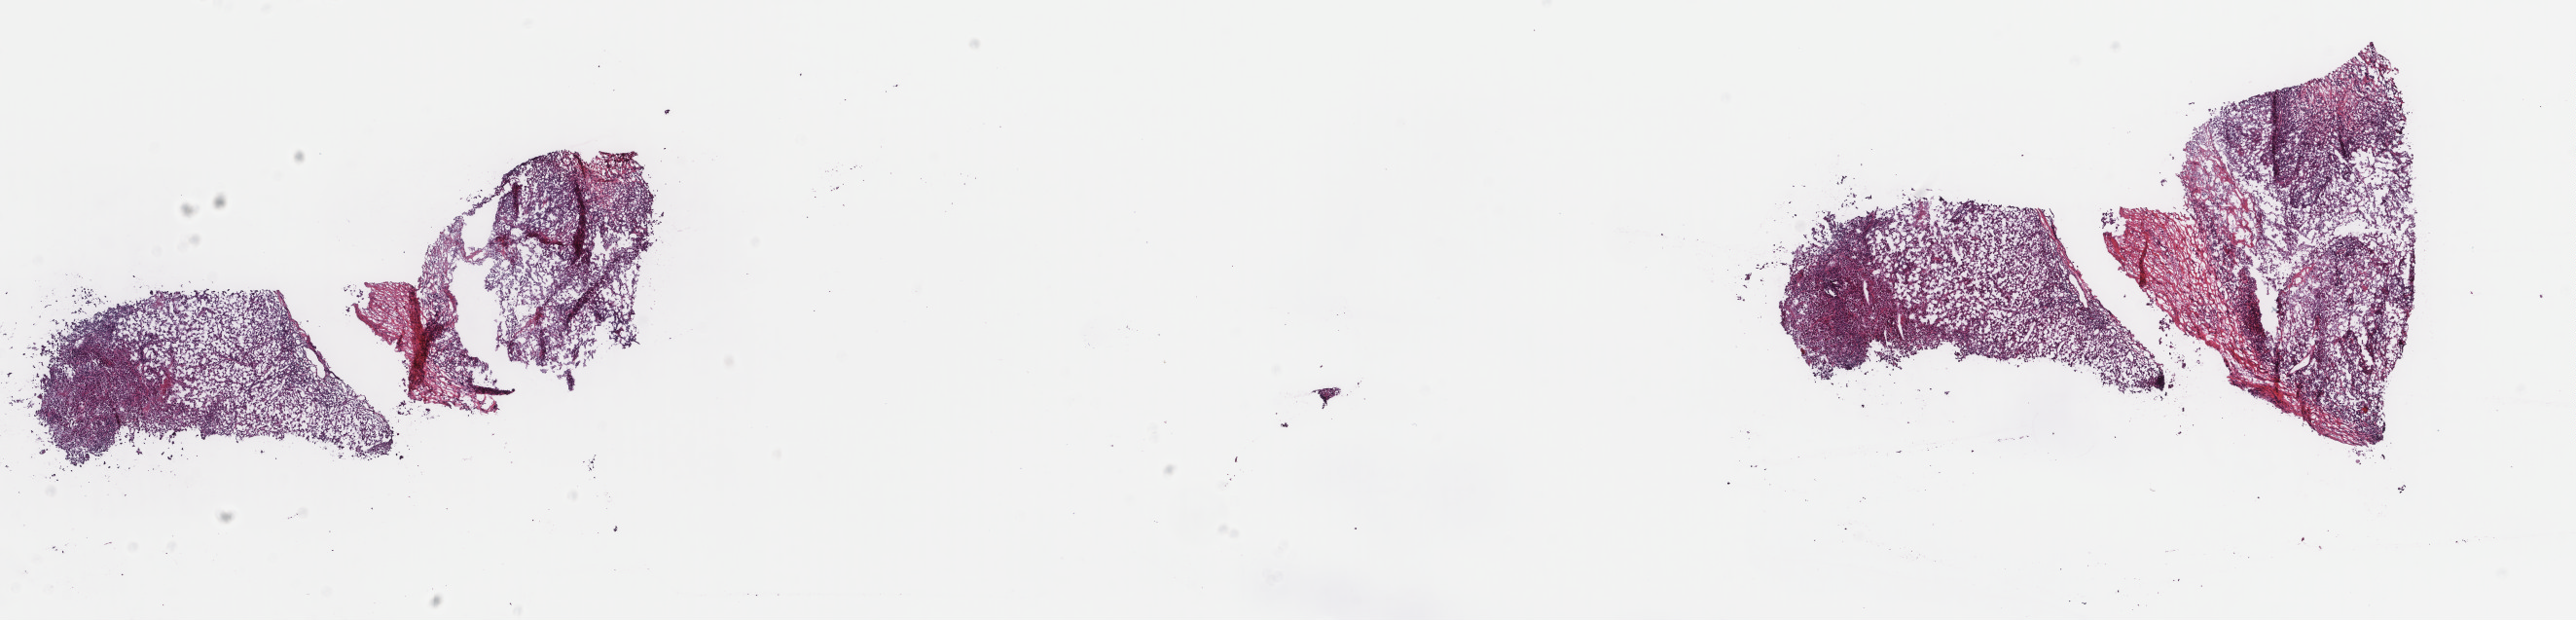
Digitized H&E tissue section (whole slide) — shown as a low-resolution overview of the whole scanned area (about 21.0 x 5.1 mm), frozen section from the top of the tissue portion, metastatic tumour sample, sampled site: connective, subcutaneous and other soft tissues. Male patient; age at initial diagnosis 42 years. Composition of this section per pathologist review: tumour cells 85%, tumour nuclei 90%.
This section: metastatic tumour tissue. Patient diagnosis: Malignant melanoma, NOS.